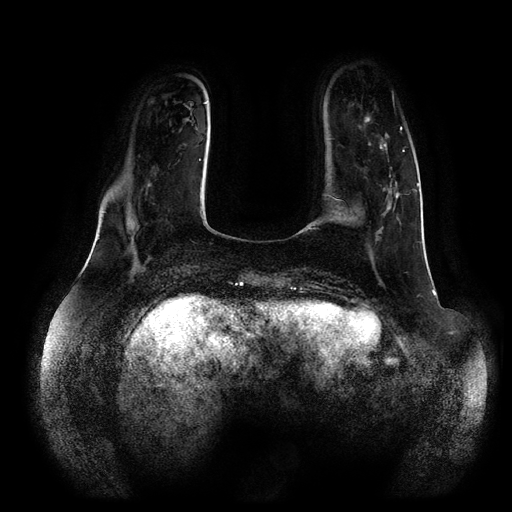
Breast MRI (dynamic contrast-enhanced, multi-phase), one axial slice; dynamic contrast-enhanced series, time point 2 of 5 at this slice position (early post-contrast); 1.5 T; TE 2.5 ms, TR 5.2 ms; 2 mm slice thickness; 512 × 512 image matrix. Patient: female, 66 years.
Outlined on this slice (semi-automatically segmented with operator editing):
- breast lesion (labelled 'tumour' in the annotation; benign lesions carry a separate 'benign' label): box from (x=364, y=117) to (x=397, y=240) px